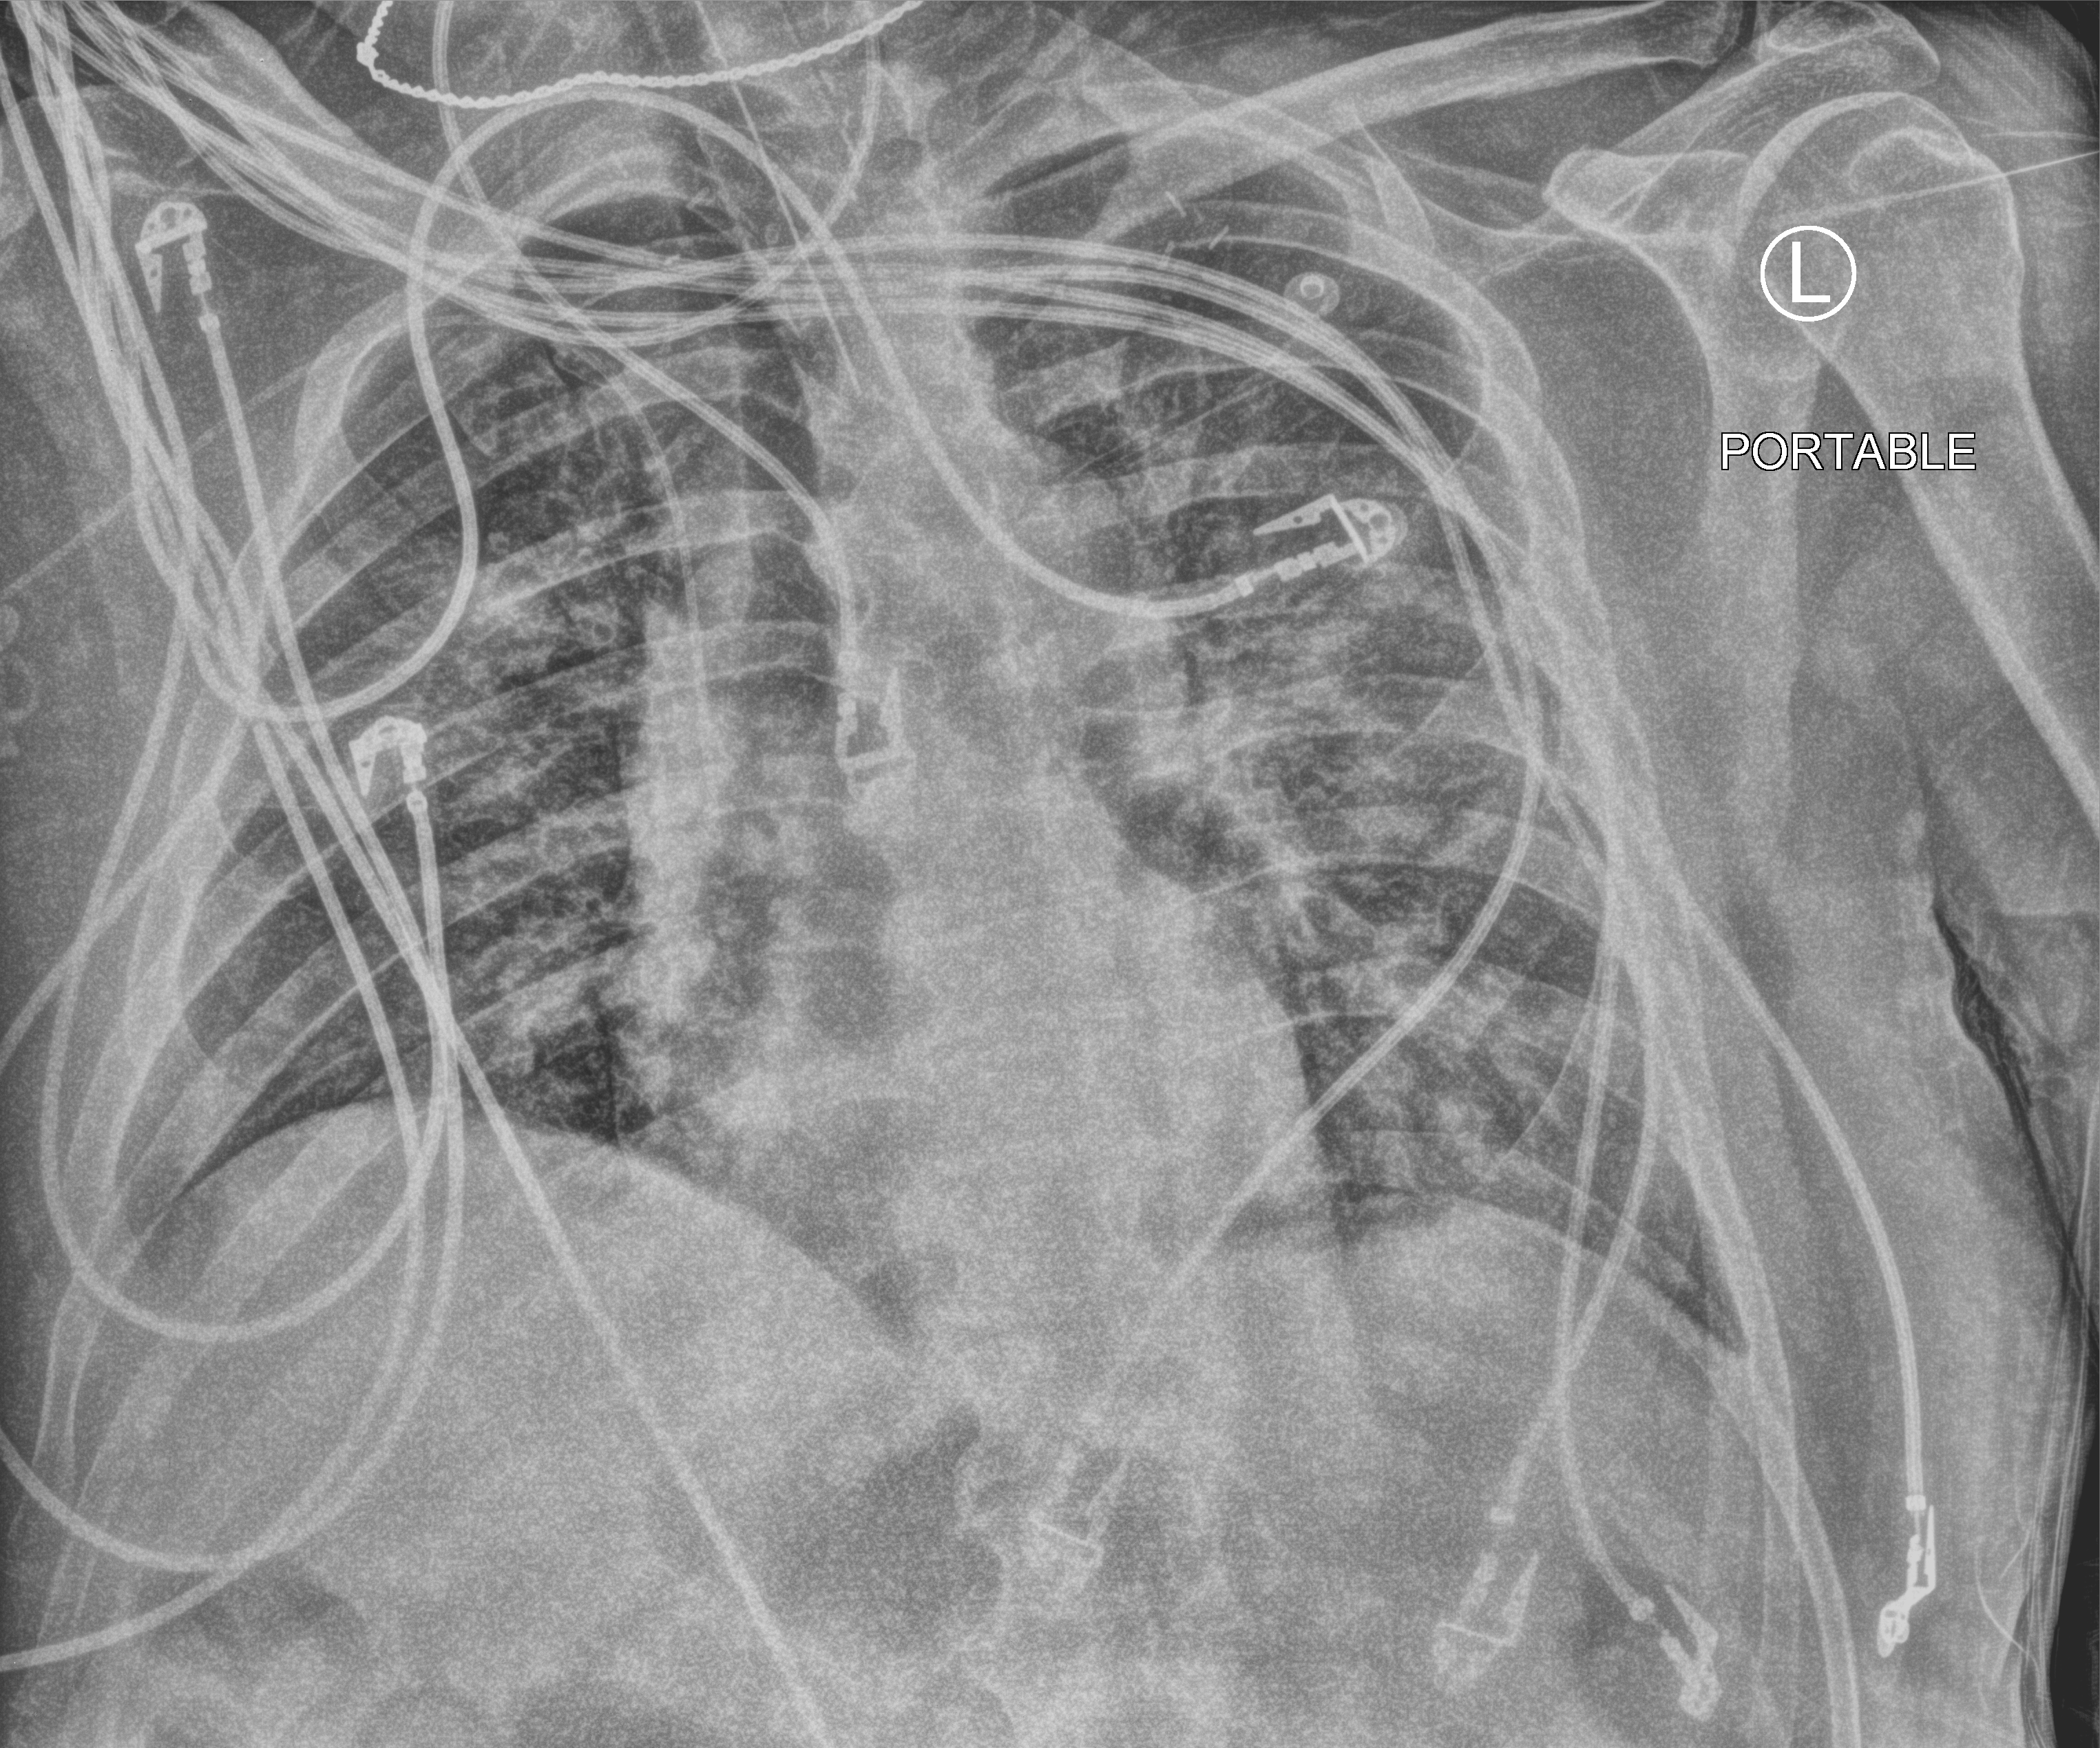
Bedside chest radiograph (computed radiography); anteroposterior (AP) projection. Patient hospitalised with COVID-19, aged 18–59 years.
Admission-level facts for this patient (not findings on this image; timing relative to this image not recorded):
- mechanically ventilated during this hospital stay: yes